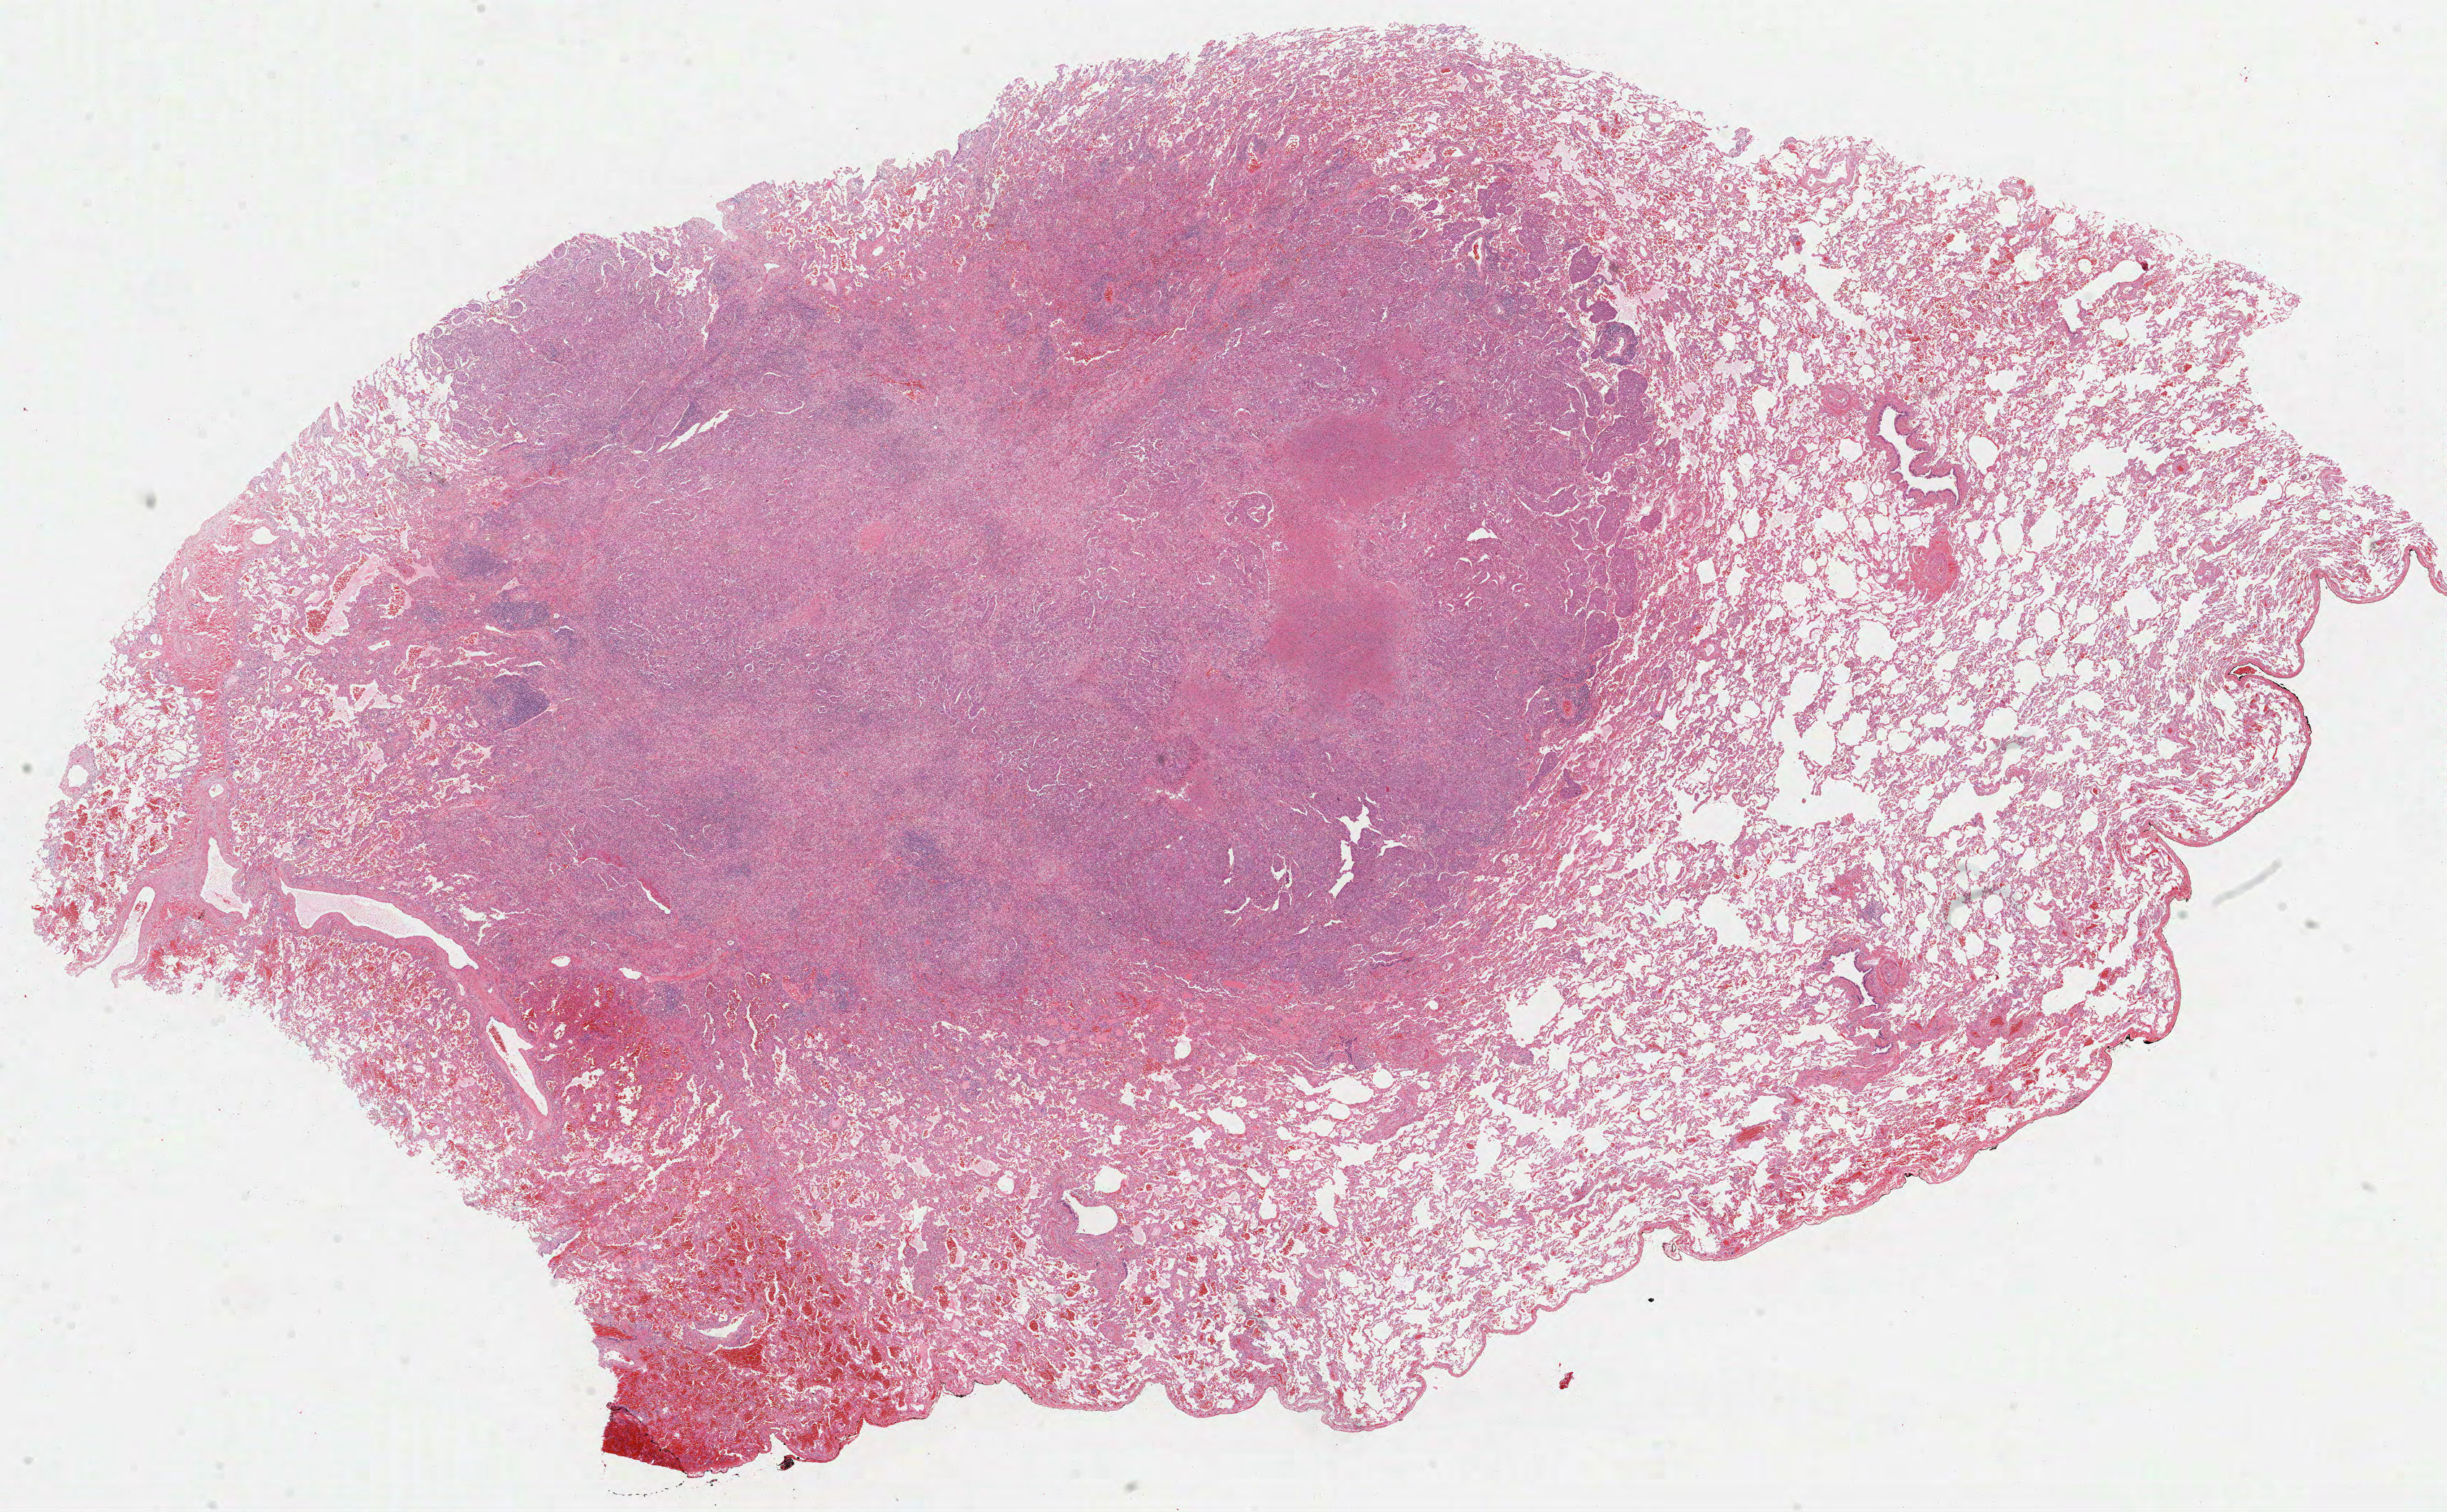
Whole-slide histology image, H&E — whole scanned area (about 27.3 x 16.9 mm, acquisition: 40x scan) shown as a low-resolution overview. FFPE section. Primary tumour sample from the lung. Female patient; age at initial diagnosis 52 years.
* TNM: T1 N0 M1
* laterality: right
* pathologic diagnosis: Adenocarcinoma, NOS (upper lobe, lung)
* AJCC pathologic stage: IV